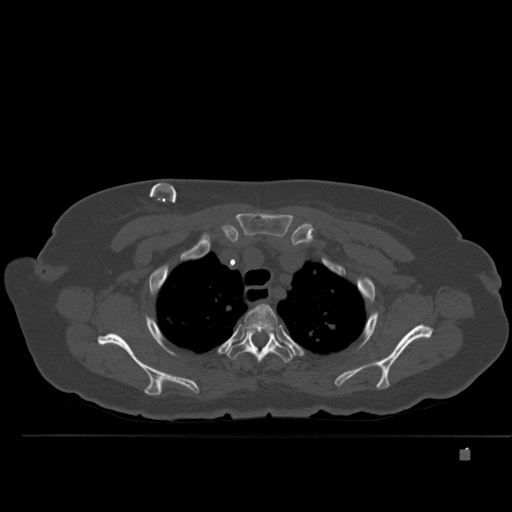
CT including the spine, one axial slice. Slice 384 of 477 in the series (ordered by position). Bone window (W 1800 / L 400 HU). 512 × 512 image matrix, field of view 422 × 422 mm. Patient: female, 74 years. From the clinical record (not read from this slice): primary cancer: colon.
Annotated regions visible in this slice (semi-automatically segmented with operator editing):
- T2 vertebra: bounding box [x1, y1, x2, y2] px = [244, 304, 278, 332]
- T3 vertebra: [227, 326, 295, 363]